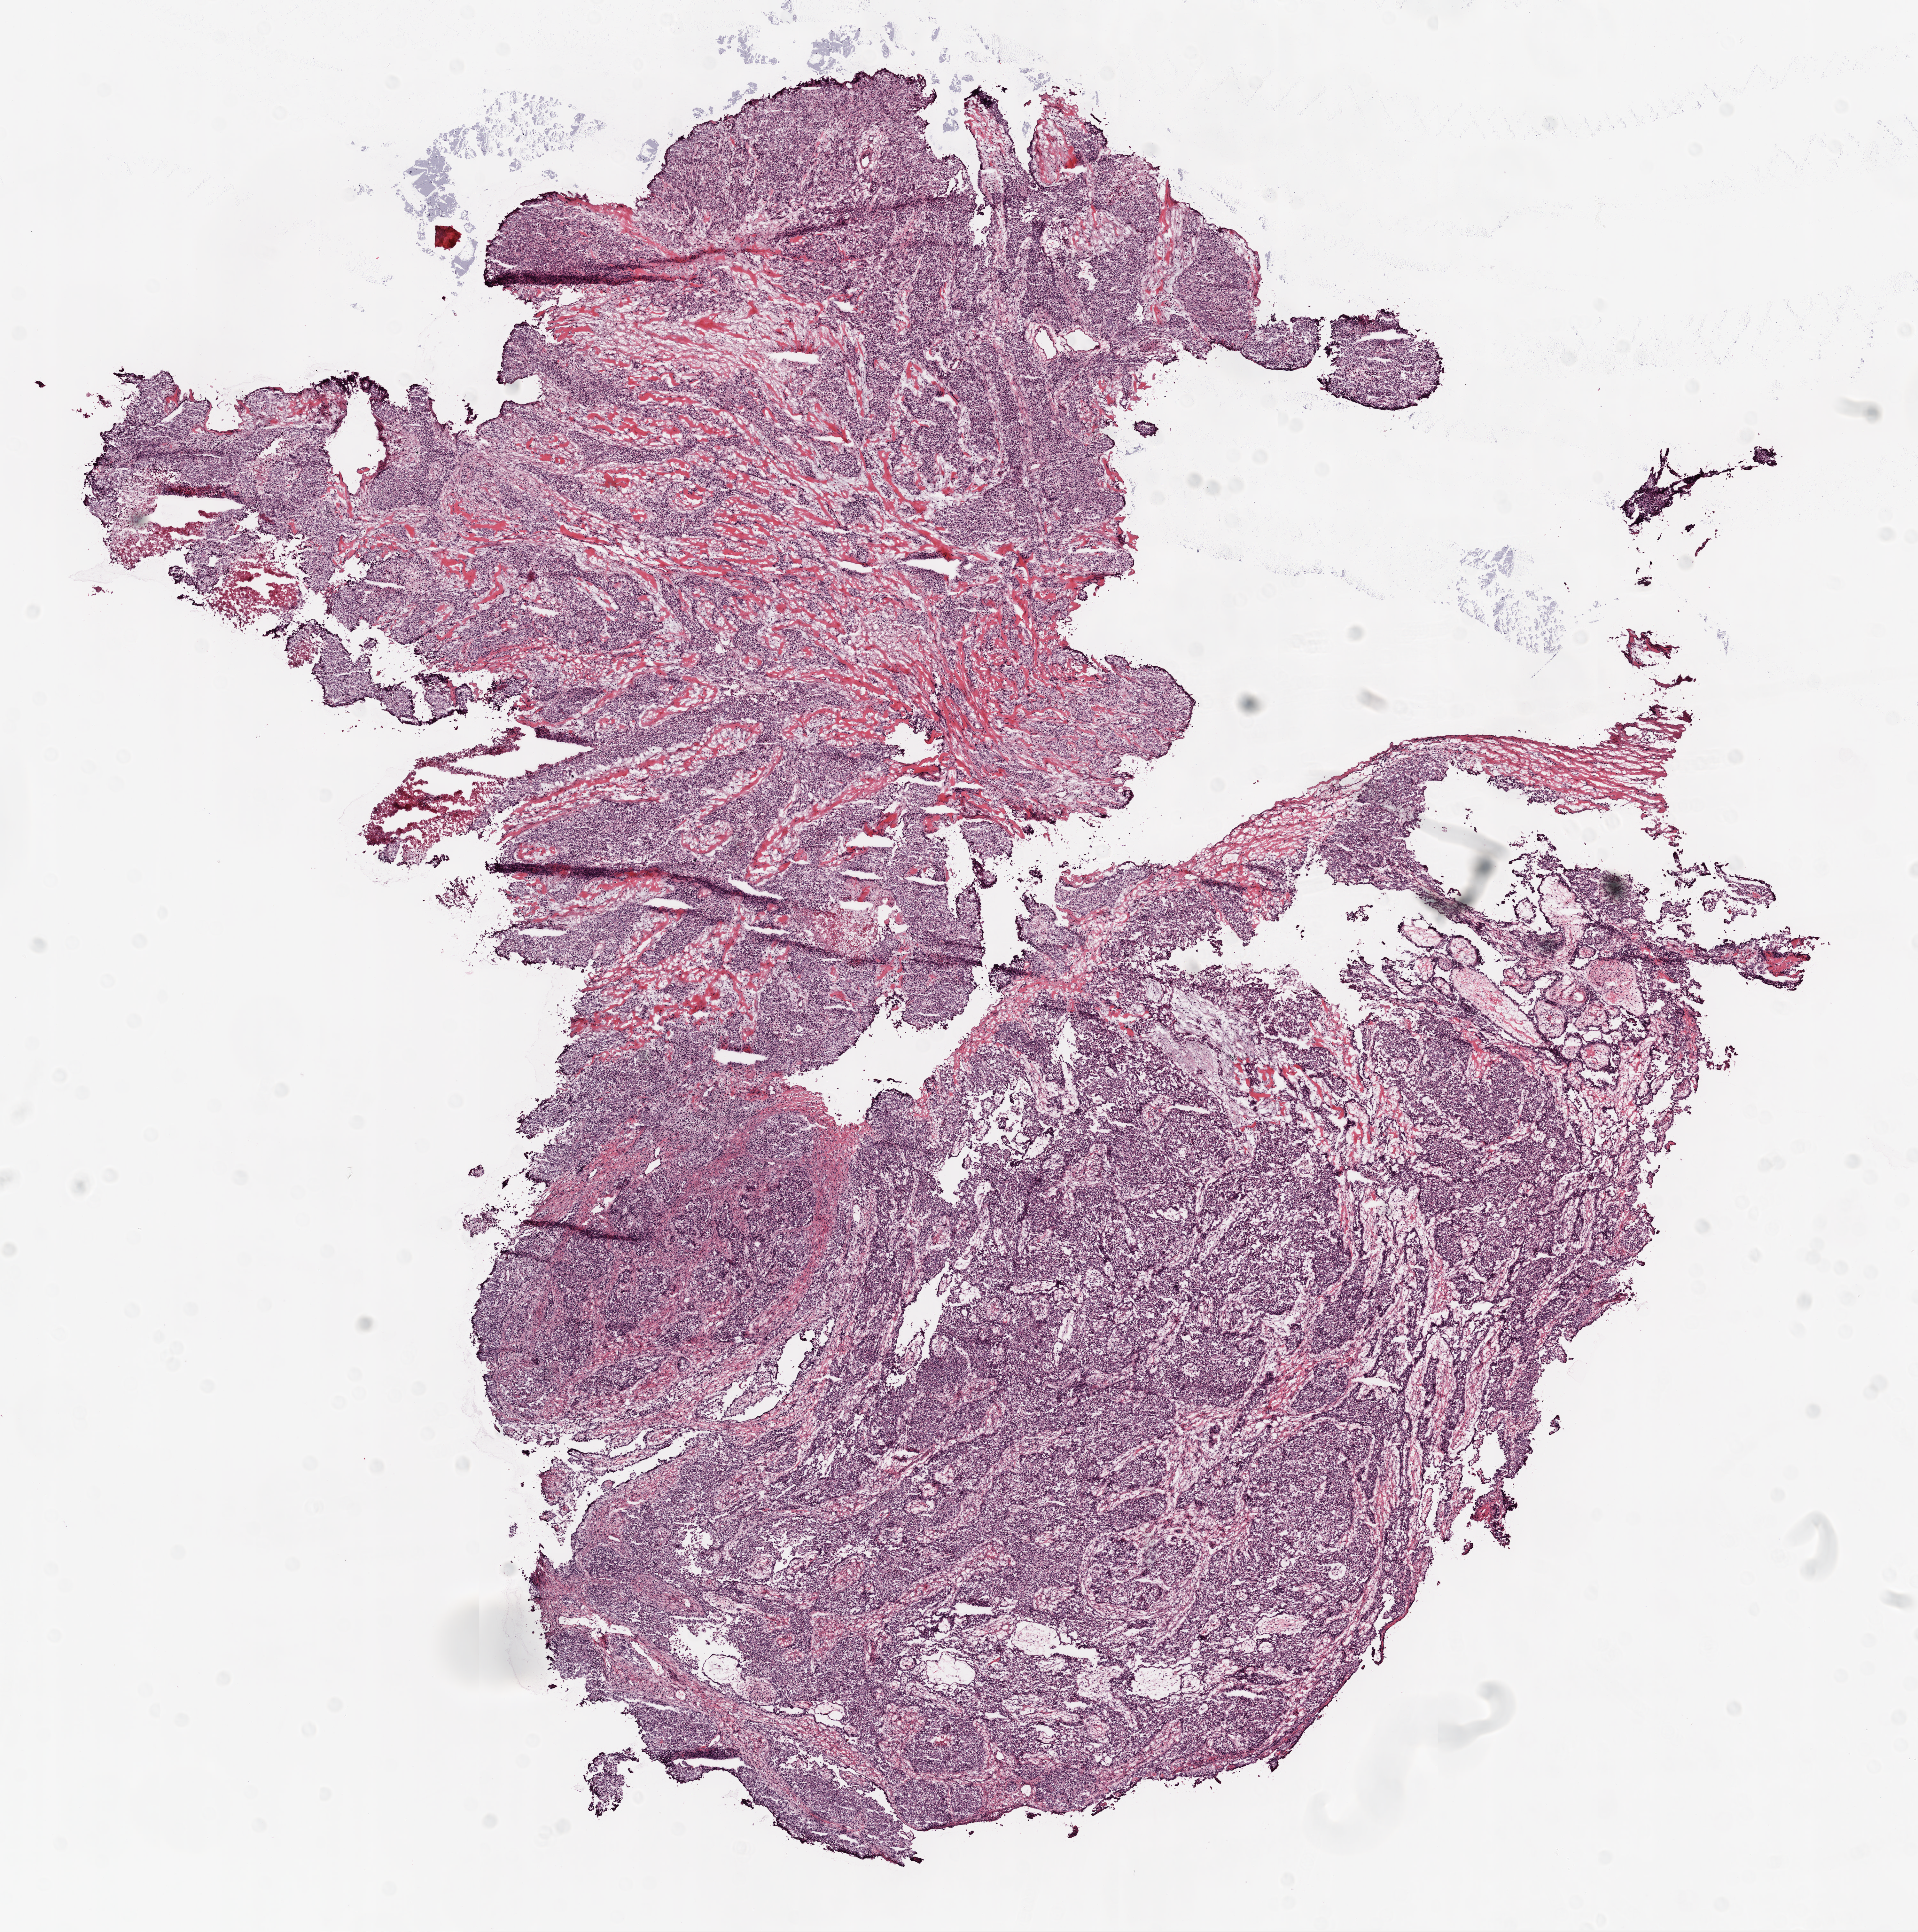
Whole-slide histology image, Hematoxylin and eosin (H&E) stained — low-resolution overview of the scanned area, about 12.0 x 12.1 mm (acquisition: 20x scan); frozen section; ovary, primary tumour sample. Patient: female, age at initial diagnosis 58 years. Histologic grade: G3 (poorly differentiated). Composition of this section per pathologist review: tumour cells 78%, tumour nuclei 90%, normal cells 0%, stromal cells 20%, necrosis 2%. Infiltration values recorded for this section: lymphocyte infiltration 5%.
Pathologic diagnosis: Serous cystadenocarcinoma, NOS. FIGO stage: IIIC. Laterality: right.